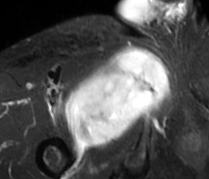
MRI of an extremity soft-tissue mass, one axial slice. Position 62 of 89 along the scan axis. STIR. MR volume resampled by the dataset authors to the PET/CT grid (not the native acquisition matrix). 3.27 mm slice thickness. 209 × 179 image matrix, field of view 204 × 175 mm. Male patient. From the clinical record (not read from this slice): histological type: undifferentiated - pleiomorphic; grade: high; site of the primary tumour: right thigh.
Outlined on this slice (expert contour drawn on MRI and transferred to this co-registered scan by the dataset authors):
- gross tumour volume including surrounding oedema: box from (x=64, y=46) to (x=168, y=150) px
- gross tumour volume (mass): (x=64, y=46)–(x=168, y=150)